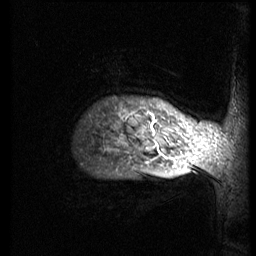
Breast MRI (dynamic contrast-enhanced), one sagittal slice. Slice 68 of 74 in the series (ordered by position). 3 images stored at this slice position (order not interpretable as contrast timing). 1.5 T. TE 4.2 ms, TR 8.9 ms. 2.5 mm slice thickness. 256 × 256 image matrix. Female patient, age 57 years. Case-level facts recorded for this patient, not image findings: setting: breast cancer imaged before/during neoadjuvant chemotherapy; receptor status: HER2-positive.
Annotated regions visible in this slice (semi-automatically segmented with operator editing):
- analysis volume of interest (the breast-tissue region the enhancement analysis was run in; not a lesion): bounding box [x1, y1, x2, y2] px = [75, 70, 248, 173]
- tumour enhancement mask (voxels above the 140 % enhancement threshold inside the analysis volume of interest): [150, 113, 189, 168]